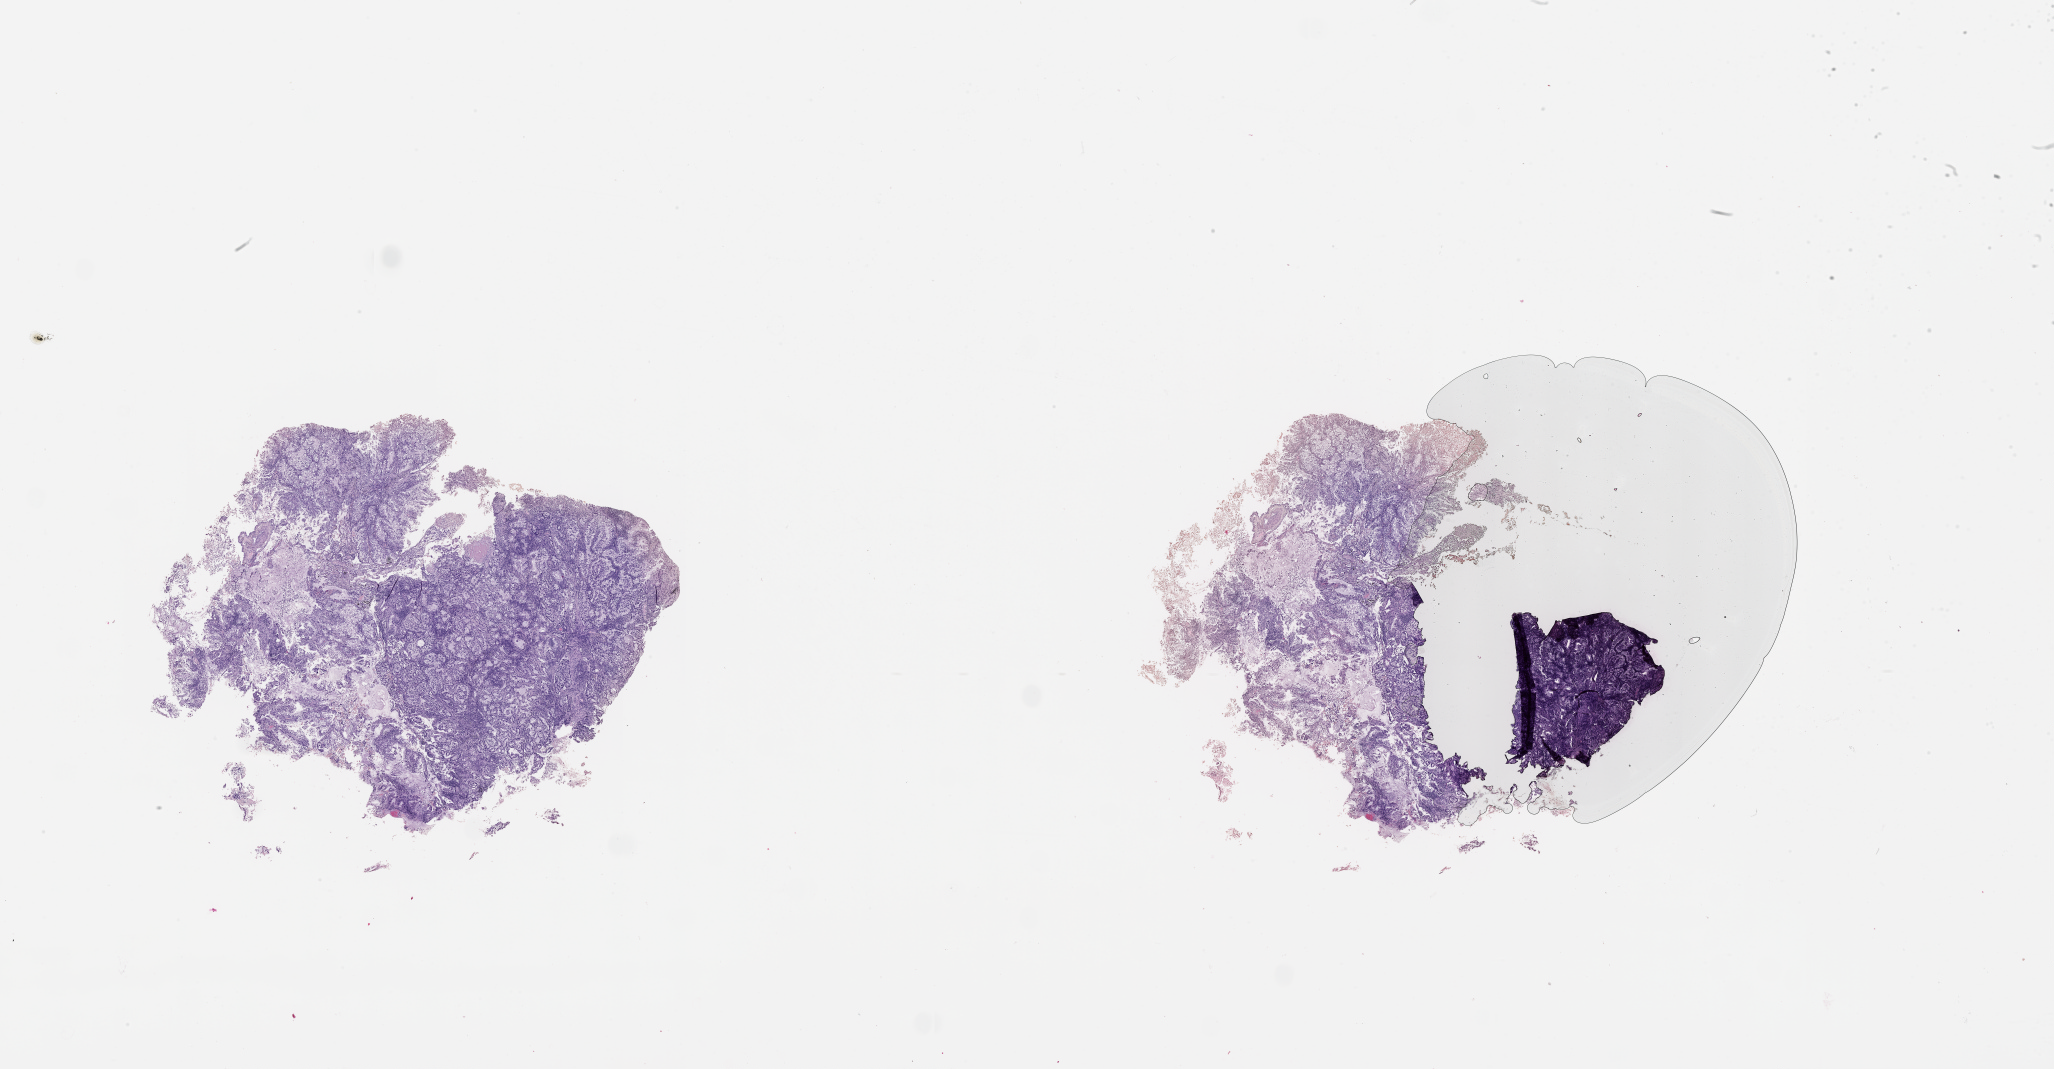
H&E whole-slide image — shown as a low-resolution overview of the whole scanned area (about 33.1 x 17.2 mm, slide scanned at 20x), tumour tissue sample, lung. Male, 67 y/o. Histologic grade: G2 (moderately differentiated).
* AJCC pathologic stage: IA
* histologic diagnosis: Adenocarcinoma, NOS